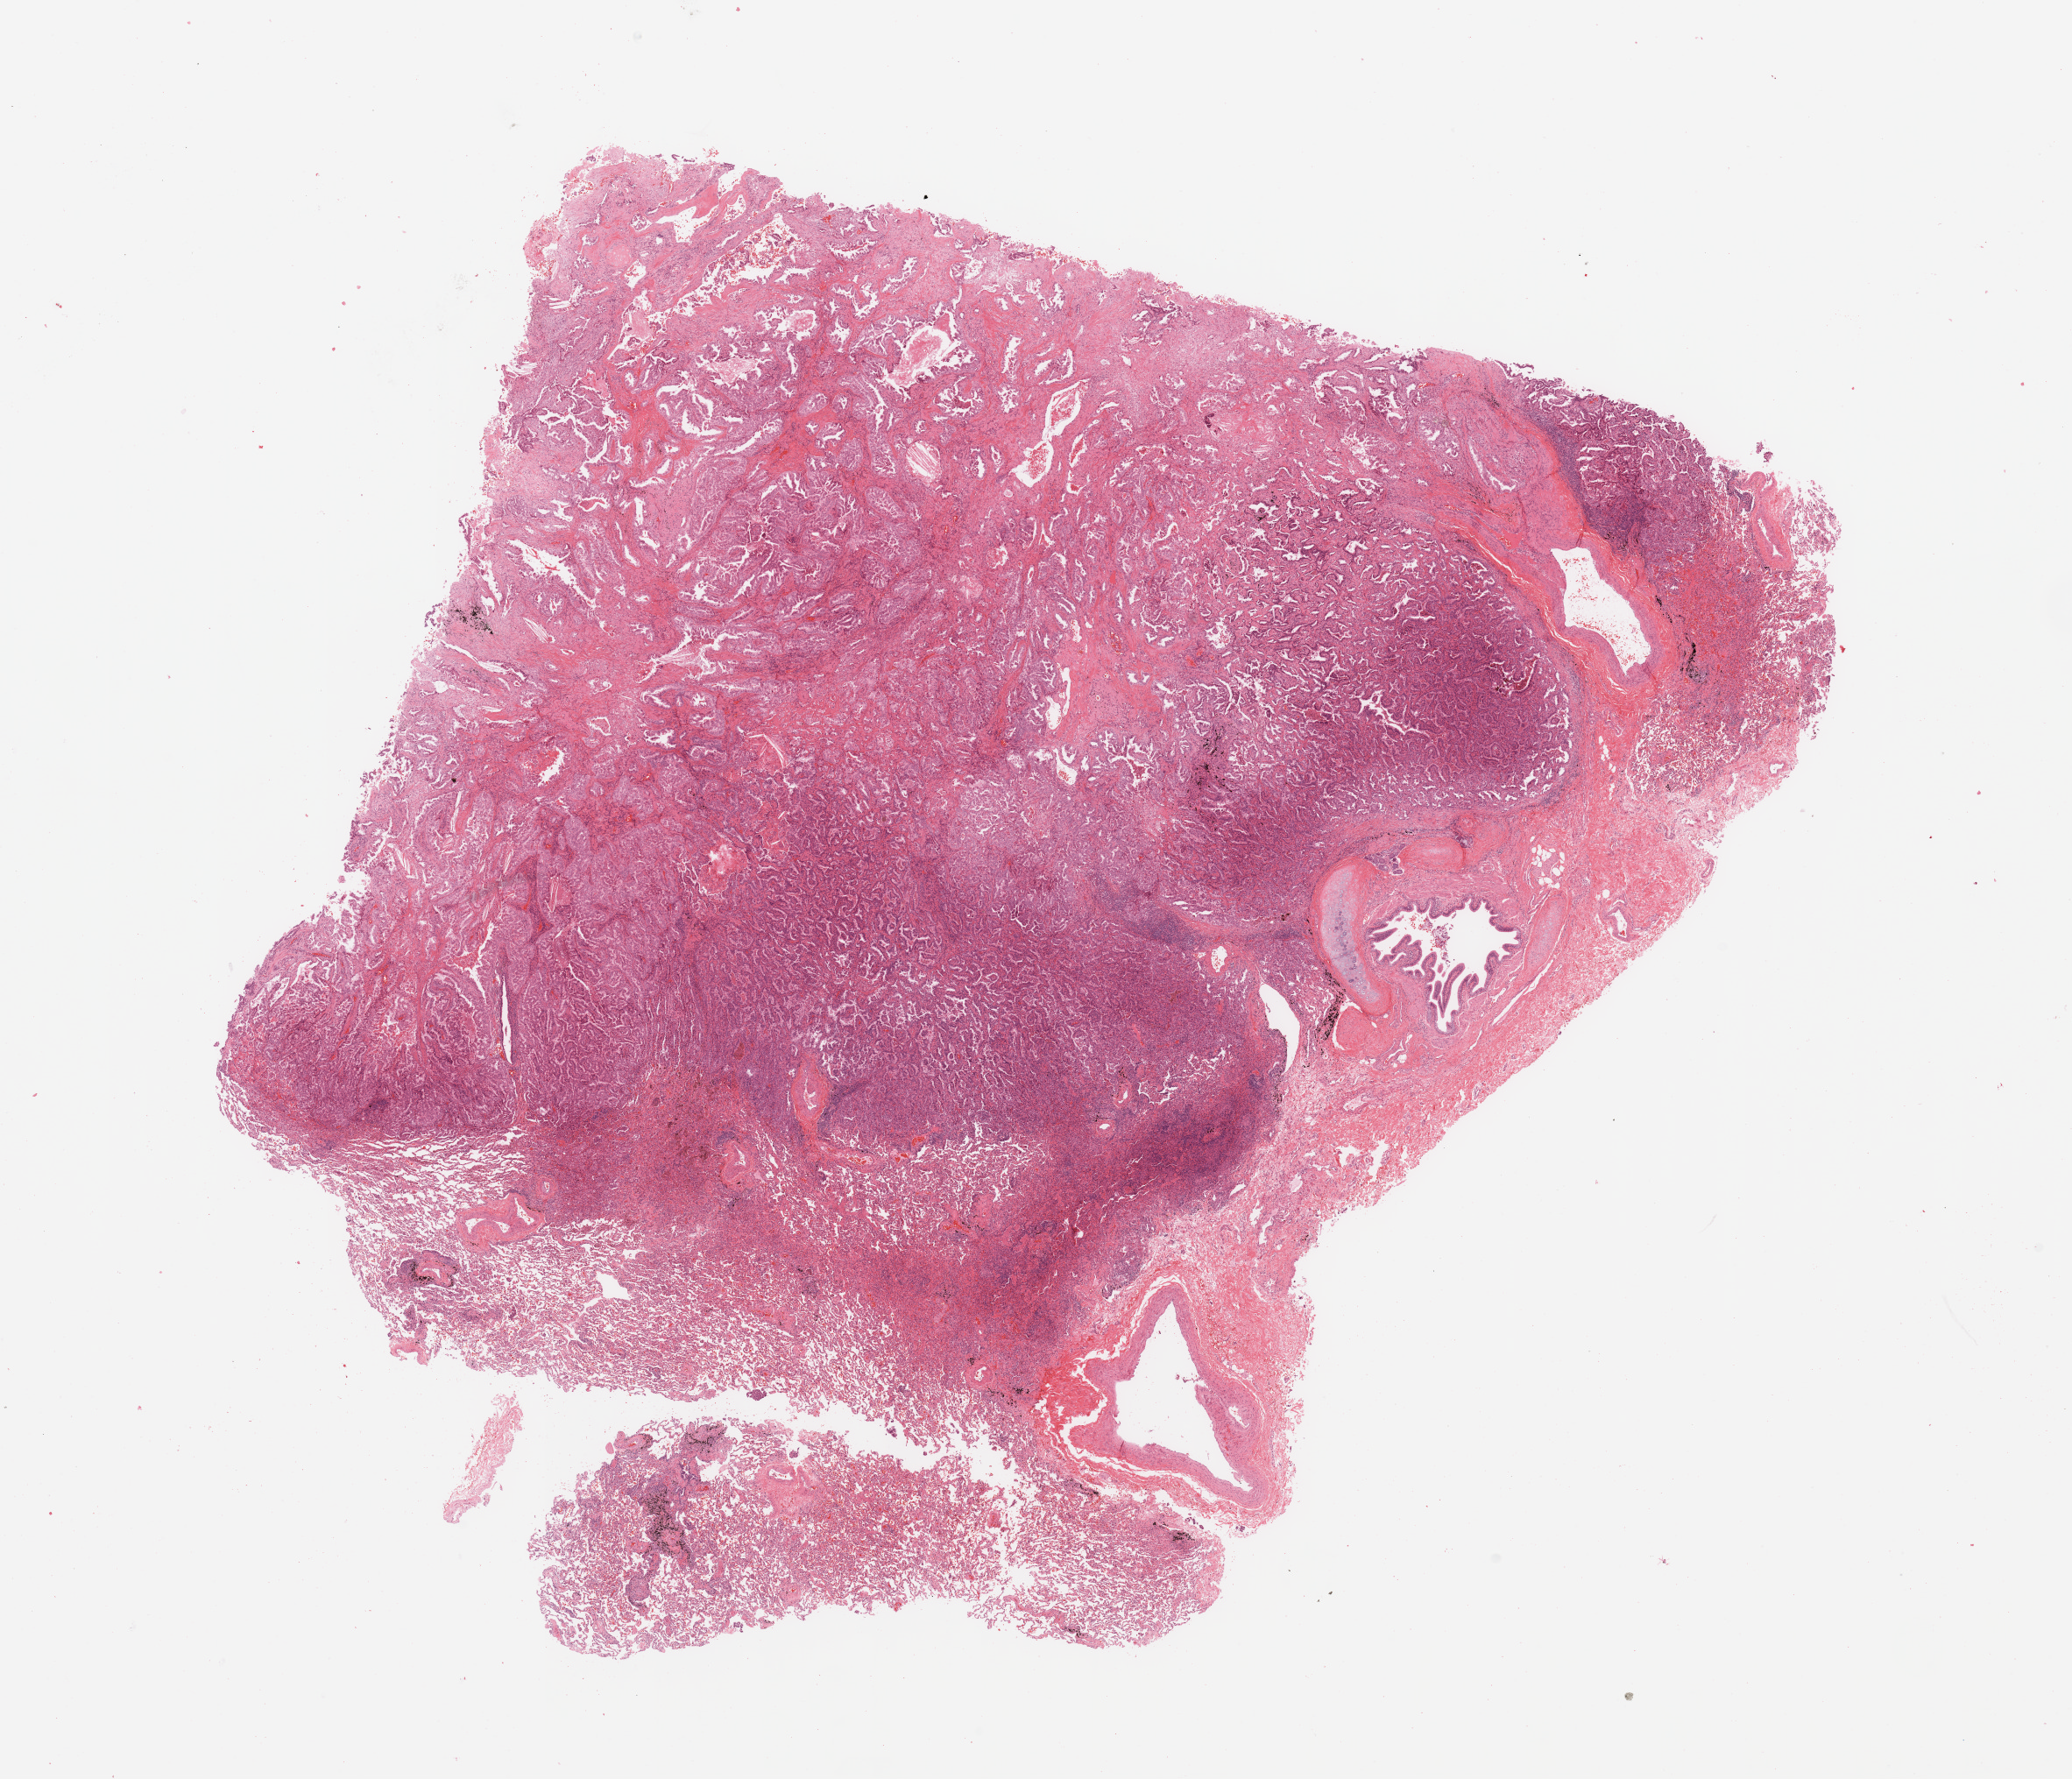
Whole-slide histology image, Hematoxylin and eosin (H&E) stained, whole scanned area (about 18.7 x 16.1 mm, from a 20x scan) shown as a low-resolution overview. Tumour tissue sample, lung. Female, 44 y/o. Histologic grade: G2 (moderately differentiated).
AJCC pathologic stage: IIIA. Diagnosis: Adenocarcinoma, NOS.